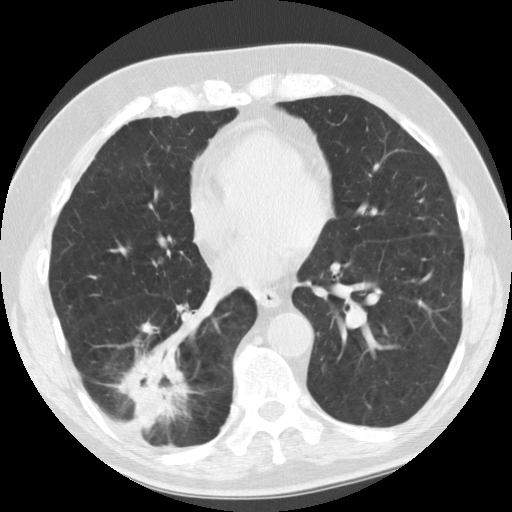
Low-dose screening chest CT, one axial slice; position 50 of 135 along the scan axis; reconstruction kernel STANDARD; 120 kVp; lung window (W 1500 / L -600 HU); 2.5 mm slice thickness; 512 × 512 image matrix, field of view 340 × 340 mm.
Annotated regions visible in this slice (manually delineated by an expert):
- lesion 1 (tumor, lower lobe of right lung): box from (x=113, y=335) to (x=192, y=438) px